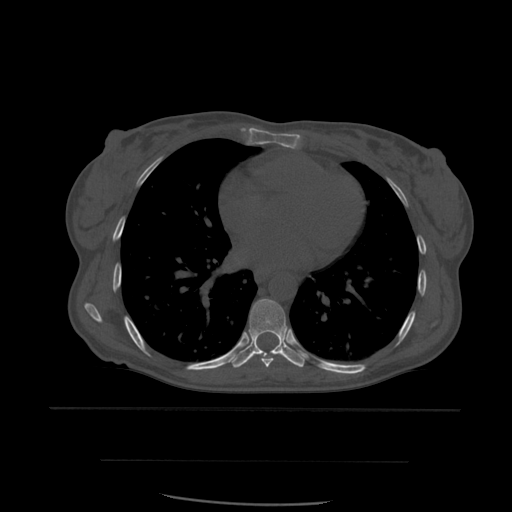
CT including the spine, one axial slice. Slice 362 of 574 in the series (ordered by position). Bone window (W 1800 / L 400 HU). 1.25 mm slice thickness. 512 × 512 image matrix, field of view 392 × 392 mm. Patient age 48 years. Case-level facts recorded for this patient, not image findings: primary cancer: lung.
Structures marked on this image (semi-automatically segmented with operator editing):
- T6 vertebra: bounding box [x1, y1, x2, y2] px = [249, 332, 253, 338]
- T7 vertebra: [261, 354, 274, 368]
- T8 vertebra: [232, 299, 306, 368]